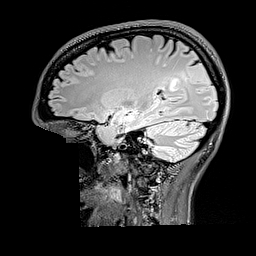
Brain MRI from a brain-tumour surgery series, one sagittal slice; position 111 of 176 along the scan axis; T2 FLAIR; 1 mm slice thickness; 256 × 256 image matrix, field of view 256 × 256 mm. From the clinical record (not read from this slice): histopathology: Oligodendroglioma; WHO grade: 2; IDH mutation: yes; tumour location: Right Parietal.
Structures marked on this image (expert manual segmentation):
- tumour: bounding box [x1, y1, x2, y2] px = [169, 77, 180, 93]